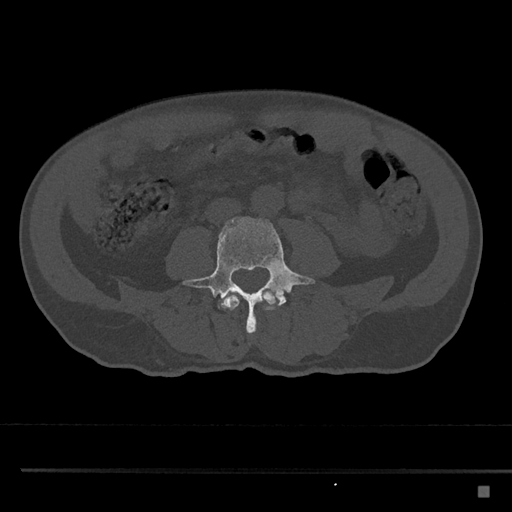
CT including the spine, one axial slice. Position 648 of 797 along the scan axis. Reconstruction kernel Br40s/3. 120 kVp. Bone window (W 1800 / L 400 HU). 512 × 512 image matrix, field of view 391 × 391 mm. Patient: male, 59 years. From the clinical record (not read from this slice): primary cancer: prostate.
Annotated regions visible in this slice (semi-automatically segmented with operator editing):
- L3 vertebra: box from (x=222, y=291) to (x=277, y=319) px
- L4 vertebra: (x=183, y=217)–(x=315, y=337)